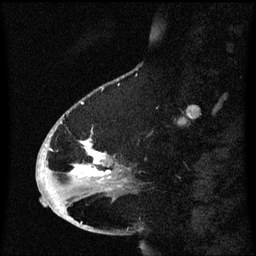
Breast MRI (dynamic contrast-enhanced), one sagittal slice. Slice 21 of 60 in the series (ordered by position). Dynamic contrast-enhanced series, image 2 of 3 at this slice position (ordered by acquisition). 1.5 T. TE 4.2 ms, TR 8.4 ms. 2.1 mm slice thickness. 256 × 256 image matrix, field of view 200 × 200 mm. Patient: female, 53 years. From the clinical record (not read from this slice): setting: breast cancer imaged before/during neoadjuvant chemotherapy; receptor status: HR-positive, HER2-negative.
Annotated regions visible in this slice (semi-automatically segmented with operator editing):
- analysis volume of interest (the breast-tissue region the enhancement analysis was run in; not a lesion): bounding box <49,110,131,201> (left, top, right, bottom; pixels)
- tumour enhancement mask (voxels above the 70 % enhancement threshold inside the analysis volume of interest): <72,140,112,177>